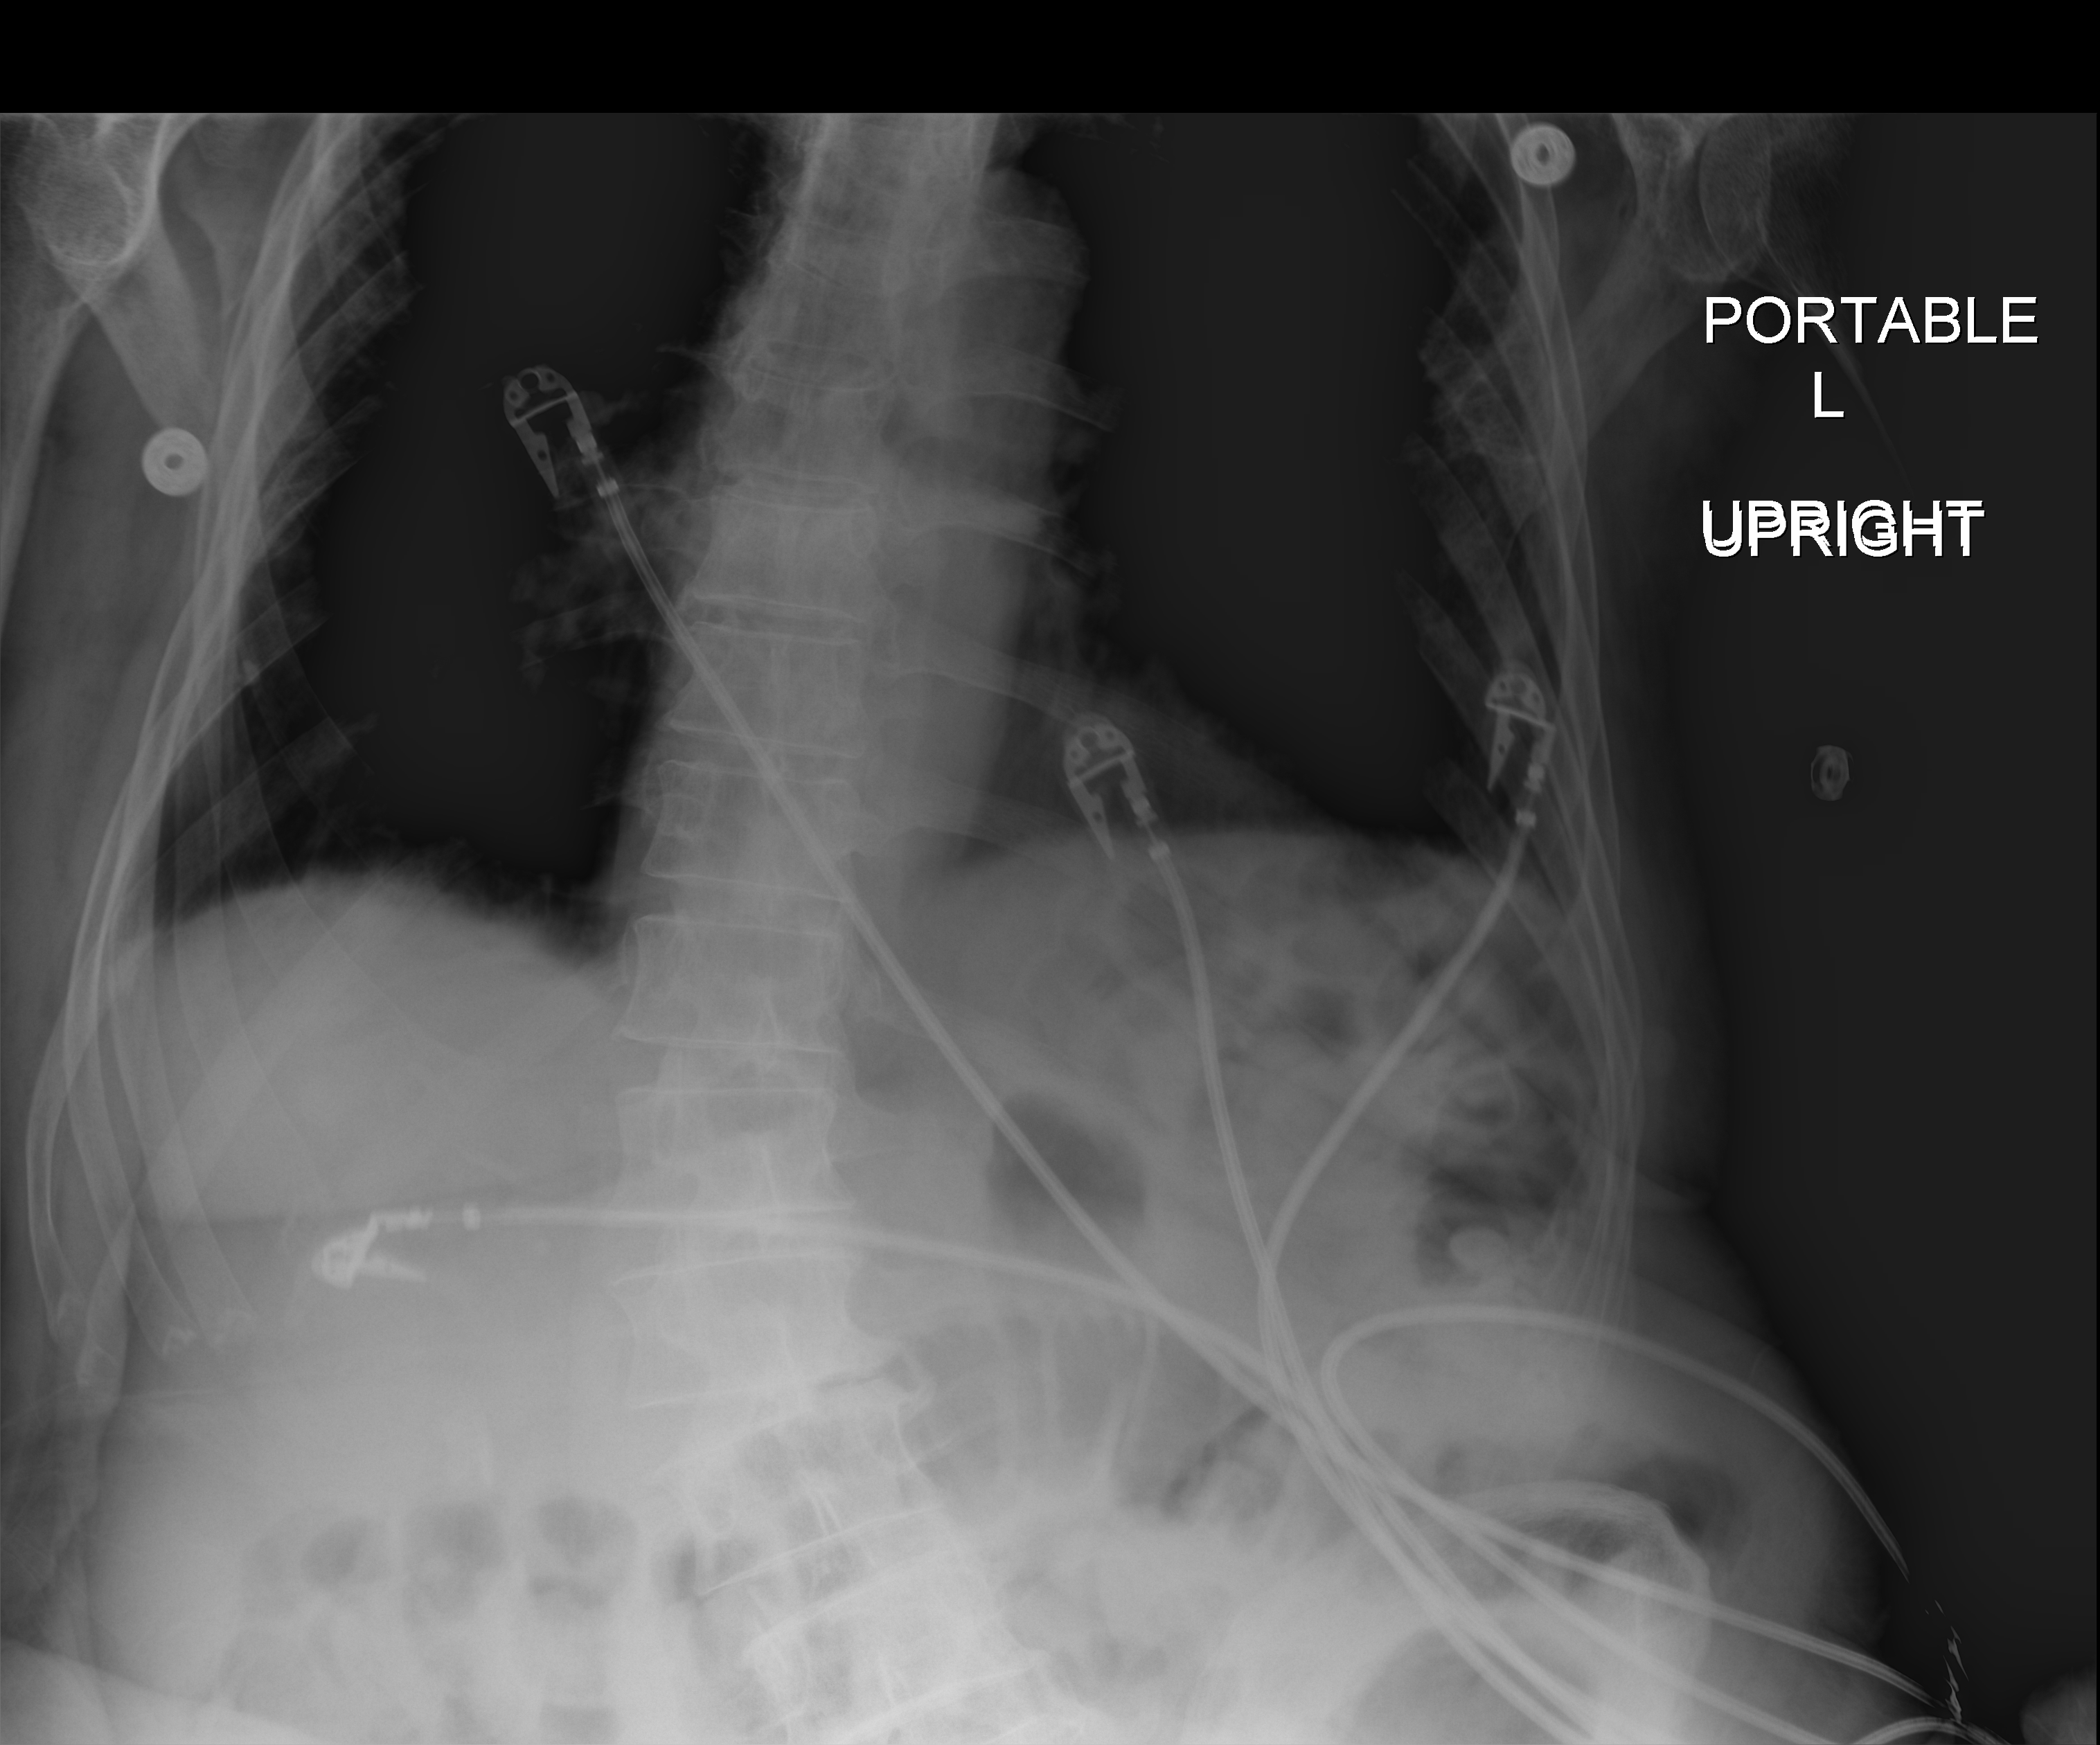
Bedside abdomen radiograph (digital radiography); anteroposterior (AP) projection. Patient hospitalised with COVID-19; male, aged 75–90 years.
From the hospital-stay record, not from the radiograph (when in the stay this image was taken is not recorded):
- length of hospital stay: 70 days